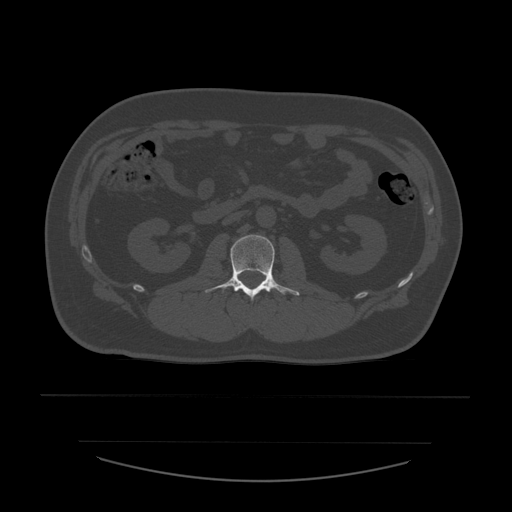
CT including the spine, one axial slice. Position 201 of 532 along the scan axis. Reconstruction kernel STANDARD. 120 kVp. Bone window (W 1800 / L 400 HU). 1.25 mm slice thickness. 512 × 512 image matrix. Patient age 44 years. From the clinical record (not read from this slice): primary cancer: soft tissue sarcoma.
Structures marked on this image (semi-automatic segmentation, software-assisted and operator-edited):
- L2 vertebra: bounding box <205,235,300,300> (left, top, right, bottom; pixels)